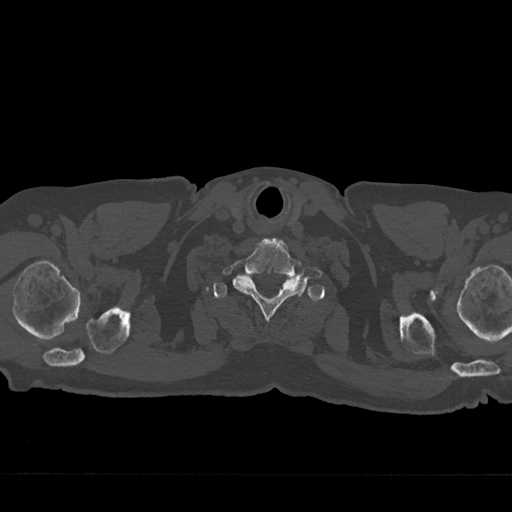
CT including the spine, one axial slice; position 685 of 797 along the scan axis; bone window (W 1800 / L 400 HU); 0.5 mm slice thickness; 512 × 512 image matrix. Male patient, age 75 years. Case-level facts recorded for this patient, not image findings: primary cancer: renal; vertebrae with lytic lesions (as recorded): T4.
Outlined on this slice (semi-automatically segmented with operator editing):
- T1 vertebra: box from (x=213, y=275) to (x=303, y=299) px